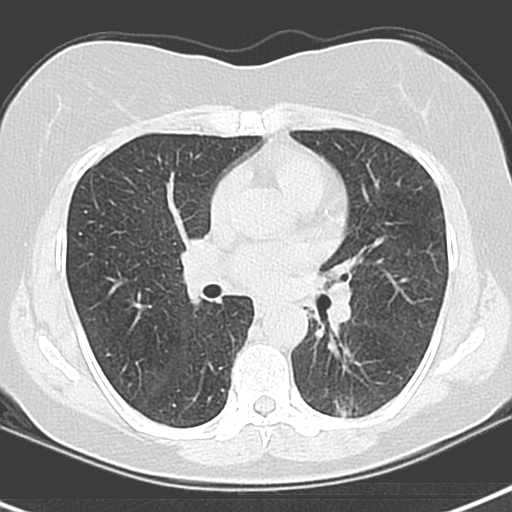
Low-dose screening chest CT, axial slice; baseline annual screen; lung window (W 1500 / L -600 HU); 3.2 mm slice thickness; standard (soft-tissue) reconstruction kernel (B); 120 kVp; slice 67 of 129 in the series. Female participant, aged 55 years at enrolment.
Lesion marked by an expert reader, bounding box (x1, y1, x2, y2) in pixels: (306, 374, 383, 424). The screening reader recorded 3 non-calcified nodules or masses ≥4 mm on this exam; which of them this box marks is not recorded. Official screen result: positive, change unspecified: nodule(s) >= 4 mm or enlarging nodule(s), mass(es), or other non-specific abnormalities suspicious for lung cancer.